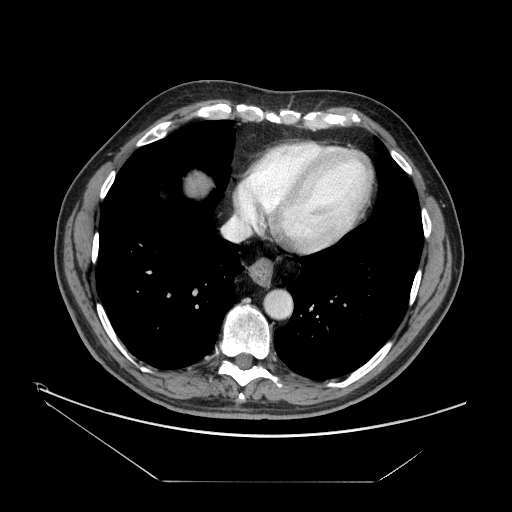
Contrast-enhanced abdominal CT, one axial slice. Position 155 of 161 along the scan axis. Reconstruction kernel STANDARD. 120 kVp. Intravenous contrast given. Soft-tissue window (W 400 / L 40 HU). 2.5 mm slice thickness. 512 × 512 image matrix, field of view 440 × 440 mm. Male patient, age 65 years. Case-level facts recorded for this patient, not image findings: diagnosis: colorectal cancer liver metastases, imaged before liver resection; multiple liver metastases: yes; largest metastasis: 4.2 cm; disease in both lobes: yes.
Annotated regions visible in this slice (manually delineated by an expert):
- hepatic veins: bounding box <222,161,267,241> (left, top, right, bottom; pixels)